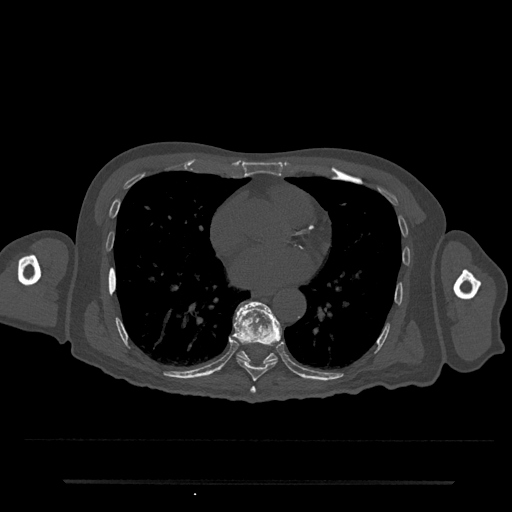
CT including the spine, one axial slice. Position 403 of 797 along the scan axis. Reconstruction kernel Br40s/3. Bone window (W 1800 / L 400 HU). 512 × 512 image matrix, field of view 427 × 427 mm. Patient: male, 74 years. Case-level facts recorded for this patient, not image findings: primary cancer: prostate.
Structures marked on this image (semi-automatically segmented with operator editing):
- T7 vertebra: bounding box (x1, y1, x2, y2) in pixels: (250, 386, 256, 394)
- T8 vertebra: (233, 301, 282, 382)
- T9 vertebra: (236, 306, 277, 364)